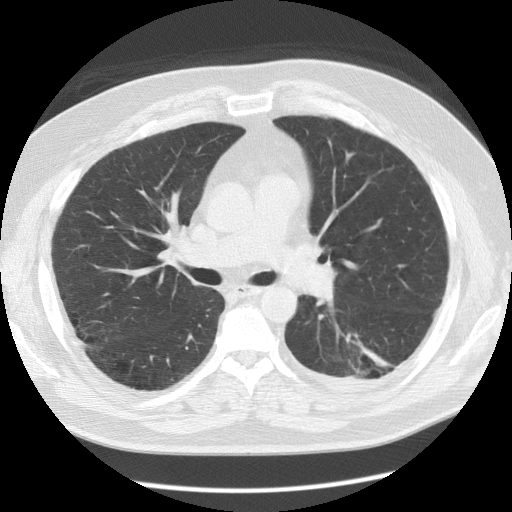
Low-dose screening chest CT, one axial slice; position 76 of 126 along the scan axis; reconstruction kernel STANDARD; 120 kVp; lung window (W 1500 / L -600 HU); 2.5 mm slice thickness; 512 × 512 image matrix, field of view 370 × 370 mm.
Outlined on this slice (expert manual segmentation):
- lesion 1 (tumor, lower lobe of left lung): bounding box (x1, y1, x2, y2) in pixels: (362, 347, 390, 367)